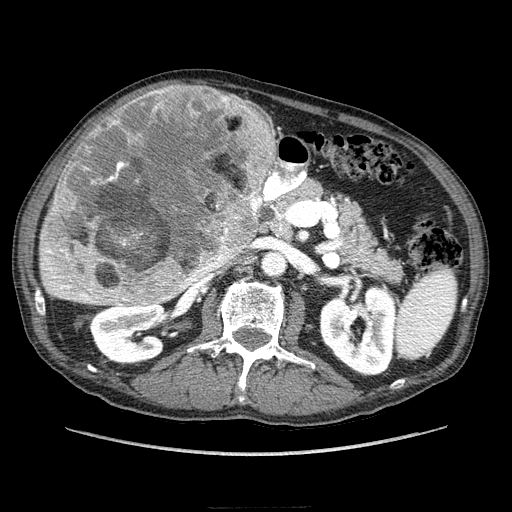
Contrast-enhanced abdominal CT (liver protocol), one axial slice. Position 115 of 218 along the scan axis. Reconstruction kernel STANDARD. 100 kVp. Soft-tissue window (W 400 / L 40 HU). 2.5 mm slice thickness. 512 × 512 image matrix, field of view 380 × 380 mm. Case-level facts recorded for this patient, not image findings: diagnosis: hepatocellular carcinoma (patient treated with transarterial chemoembolisation; whether this scan precedes or follows treatment is not stated here); TNM stage (as recorded): Stage-IIIA; Child-Pugh class: A; tumour nodularity: multinodular.
Structures marked on this image (semi-automatic segmentation, software-assisted and operator-edited):
- liver parenchyma outside the tumour (the mass and vessels are separate outlines, so this box may not span the whole liver): bounding box [x1, y1, x2, y2] px = [38, 128, 276, 304]
- mass: [44, 82, 276, 308]
- liver vessels: [48, 268, 90, 300]